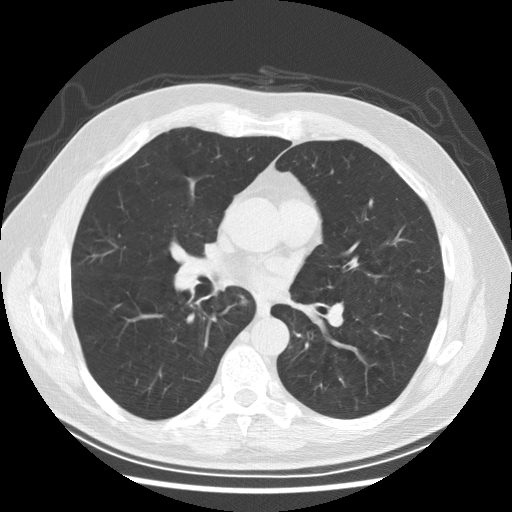
Axial slice from a low-dose chest CT screening exam; second annual screen; lung window (W 1500 / L -600 HU); 2.5 mm slice thickness; slice 120 of 246 in the series. Male participant, aged 61 years at enrolment. Former smoker at enrolment.
• Lesion marked by an expert reader, bounding box [x1, y1, x2, y2] px = [224, 282, 257, 319].
• No non-calcified nodule or mass ≥4 mm was recorded by the screening reader at this exam.